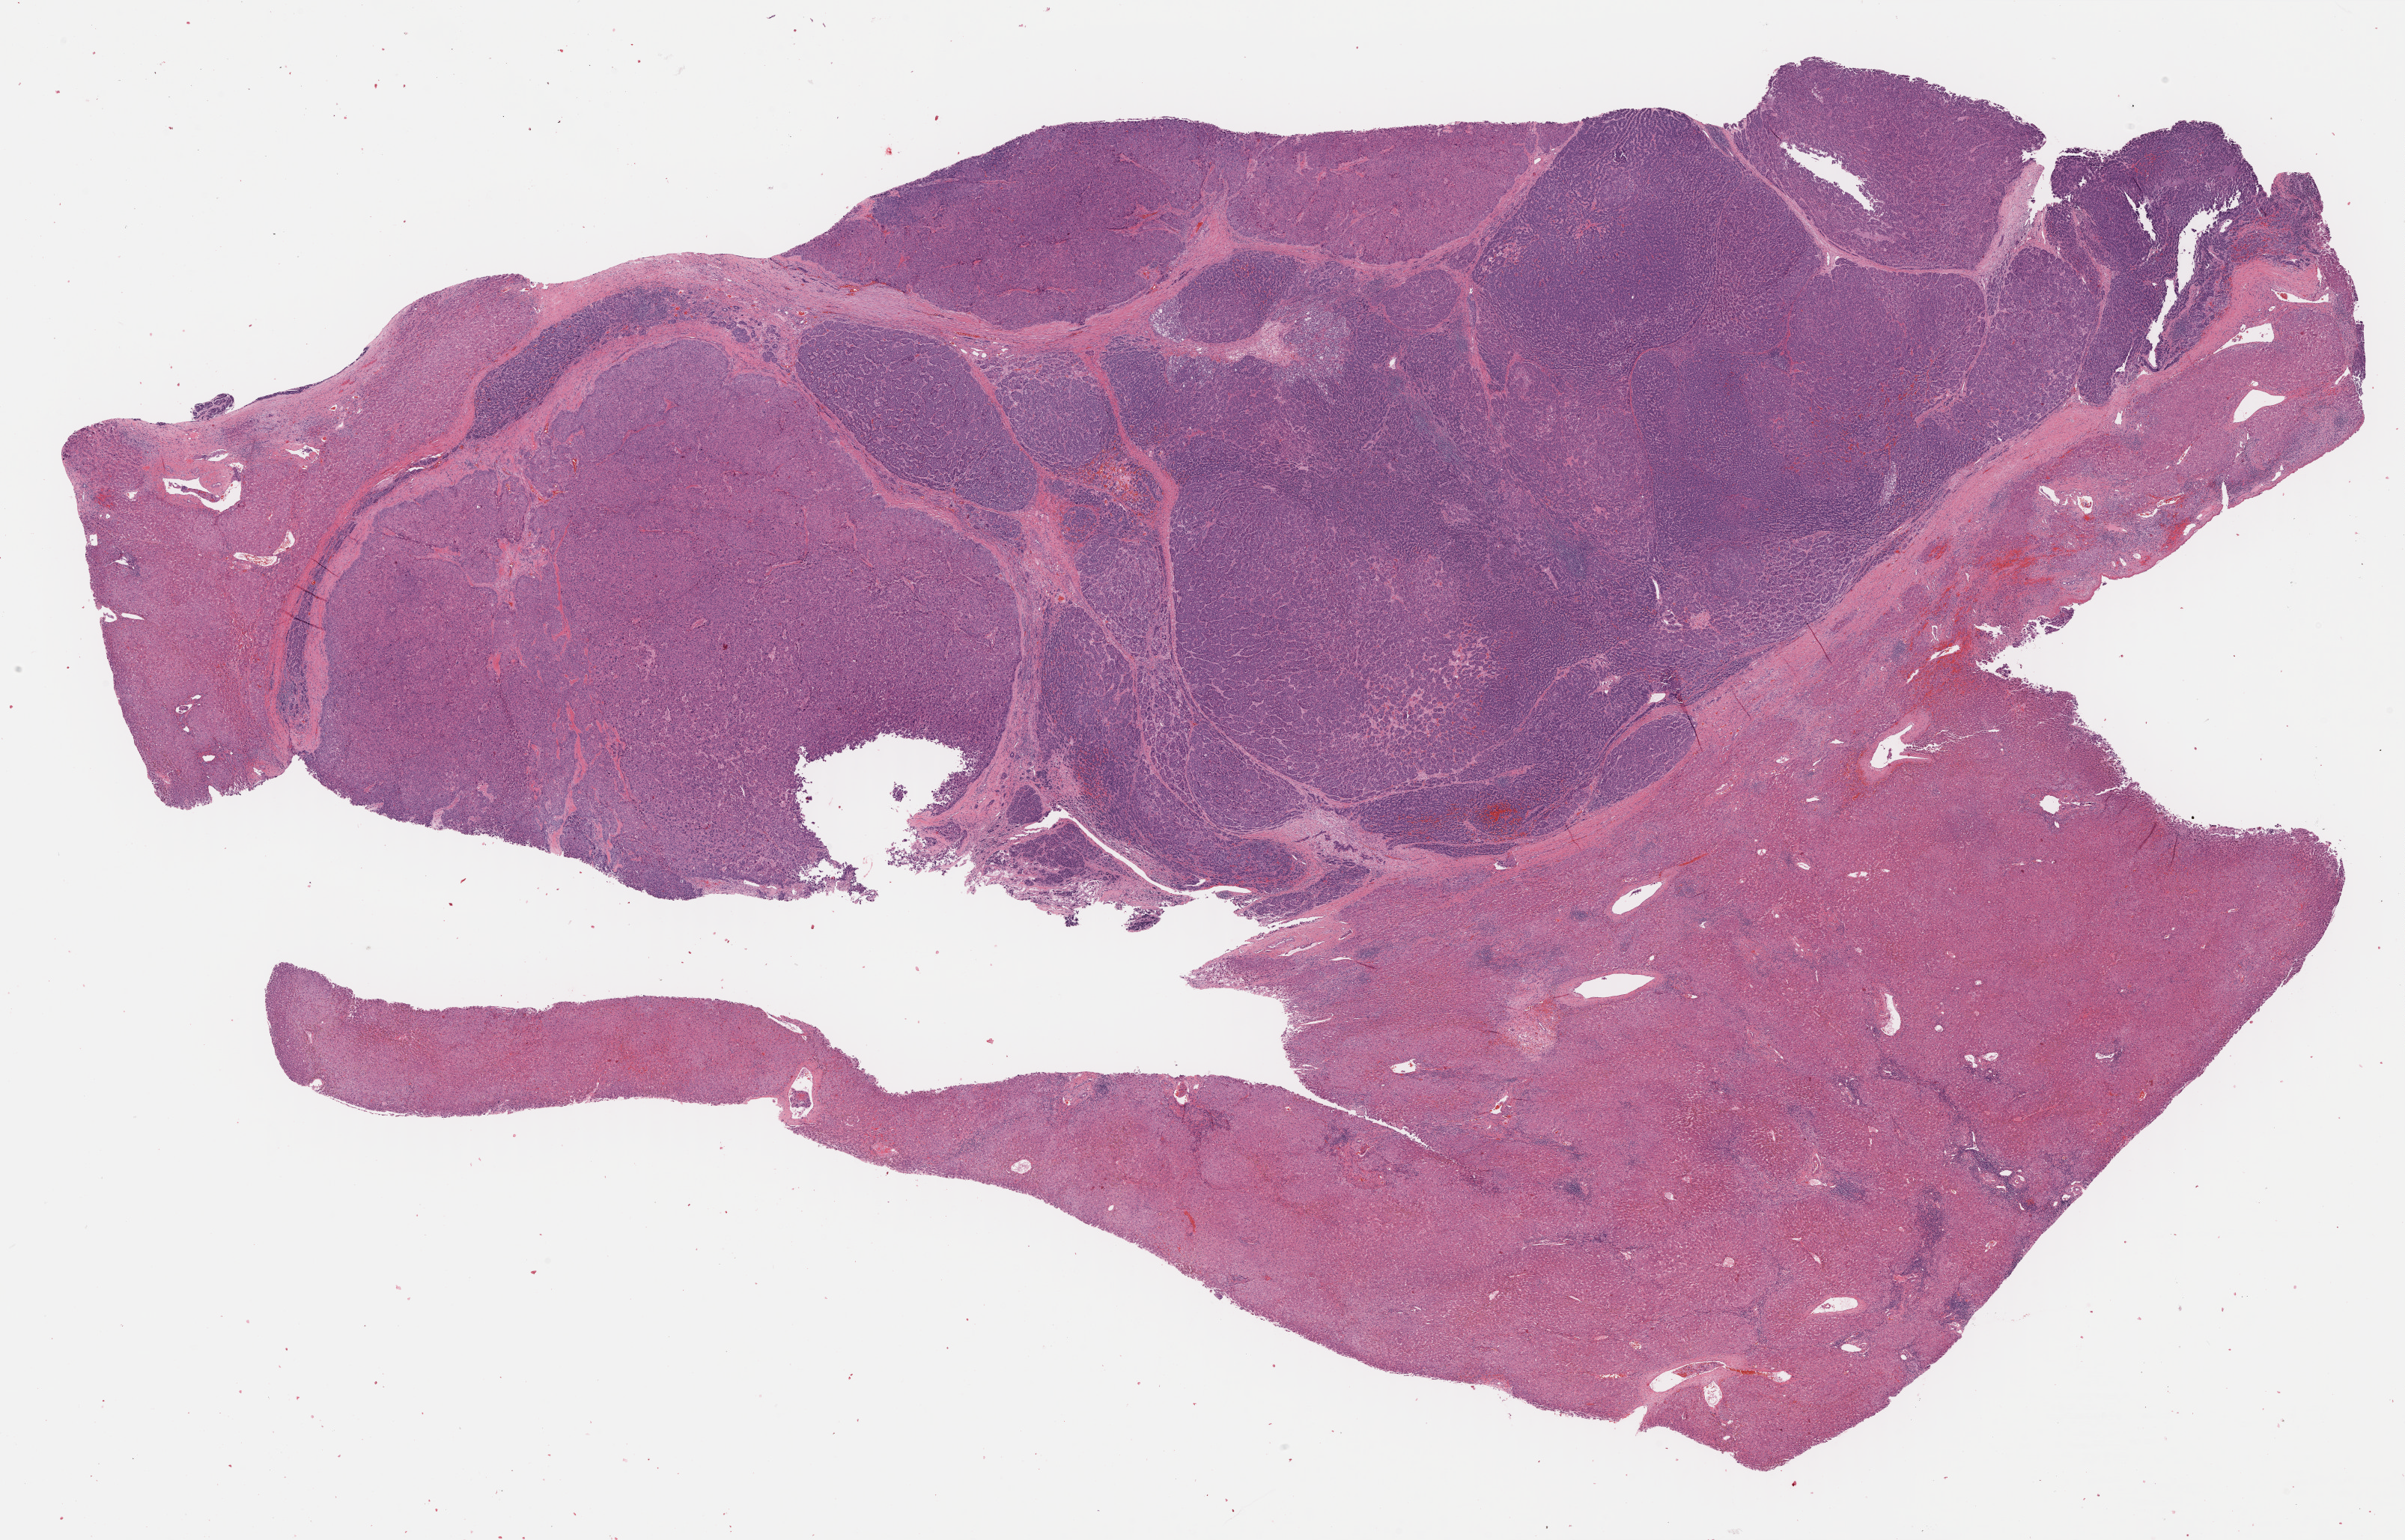
Digitized Hematoxylin and eosin (H&E) stained tissue section (whole slide) — whole scanned area (about 26.0 x 16.7 mm, slide scanned at 40x) shown as a low-resolution overview. Formalin-fixed paraffin-embedded (FFPE) diagnostic section. Sample: primary tumour, liver. Female patient; age at initial diagnosis 55 years. Histologic grade: G3 (poorly differentiated).
Diagnosis: Hepatocellular carcinoma, NOS. AJCC pathologic stage: II (6th edition).